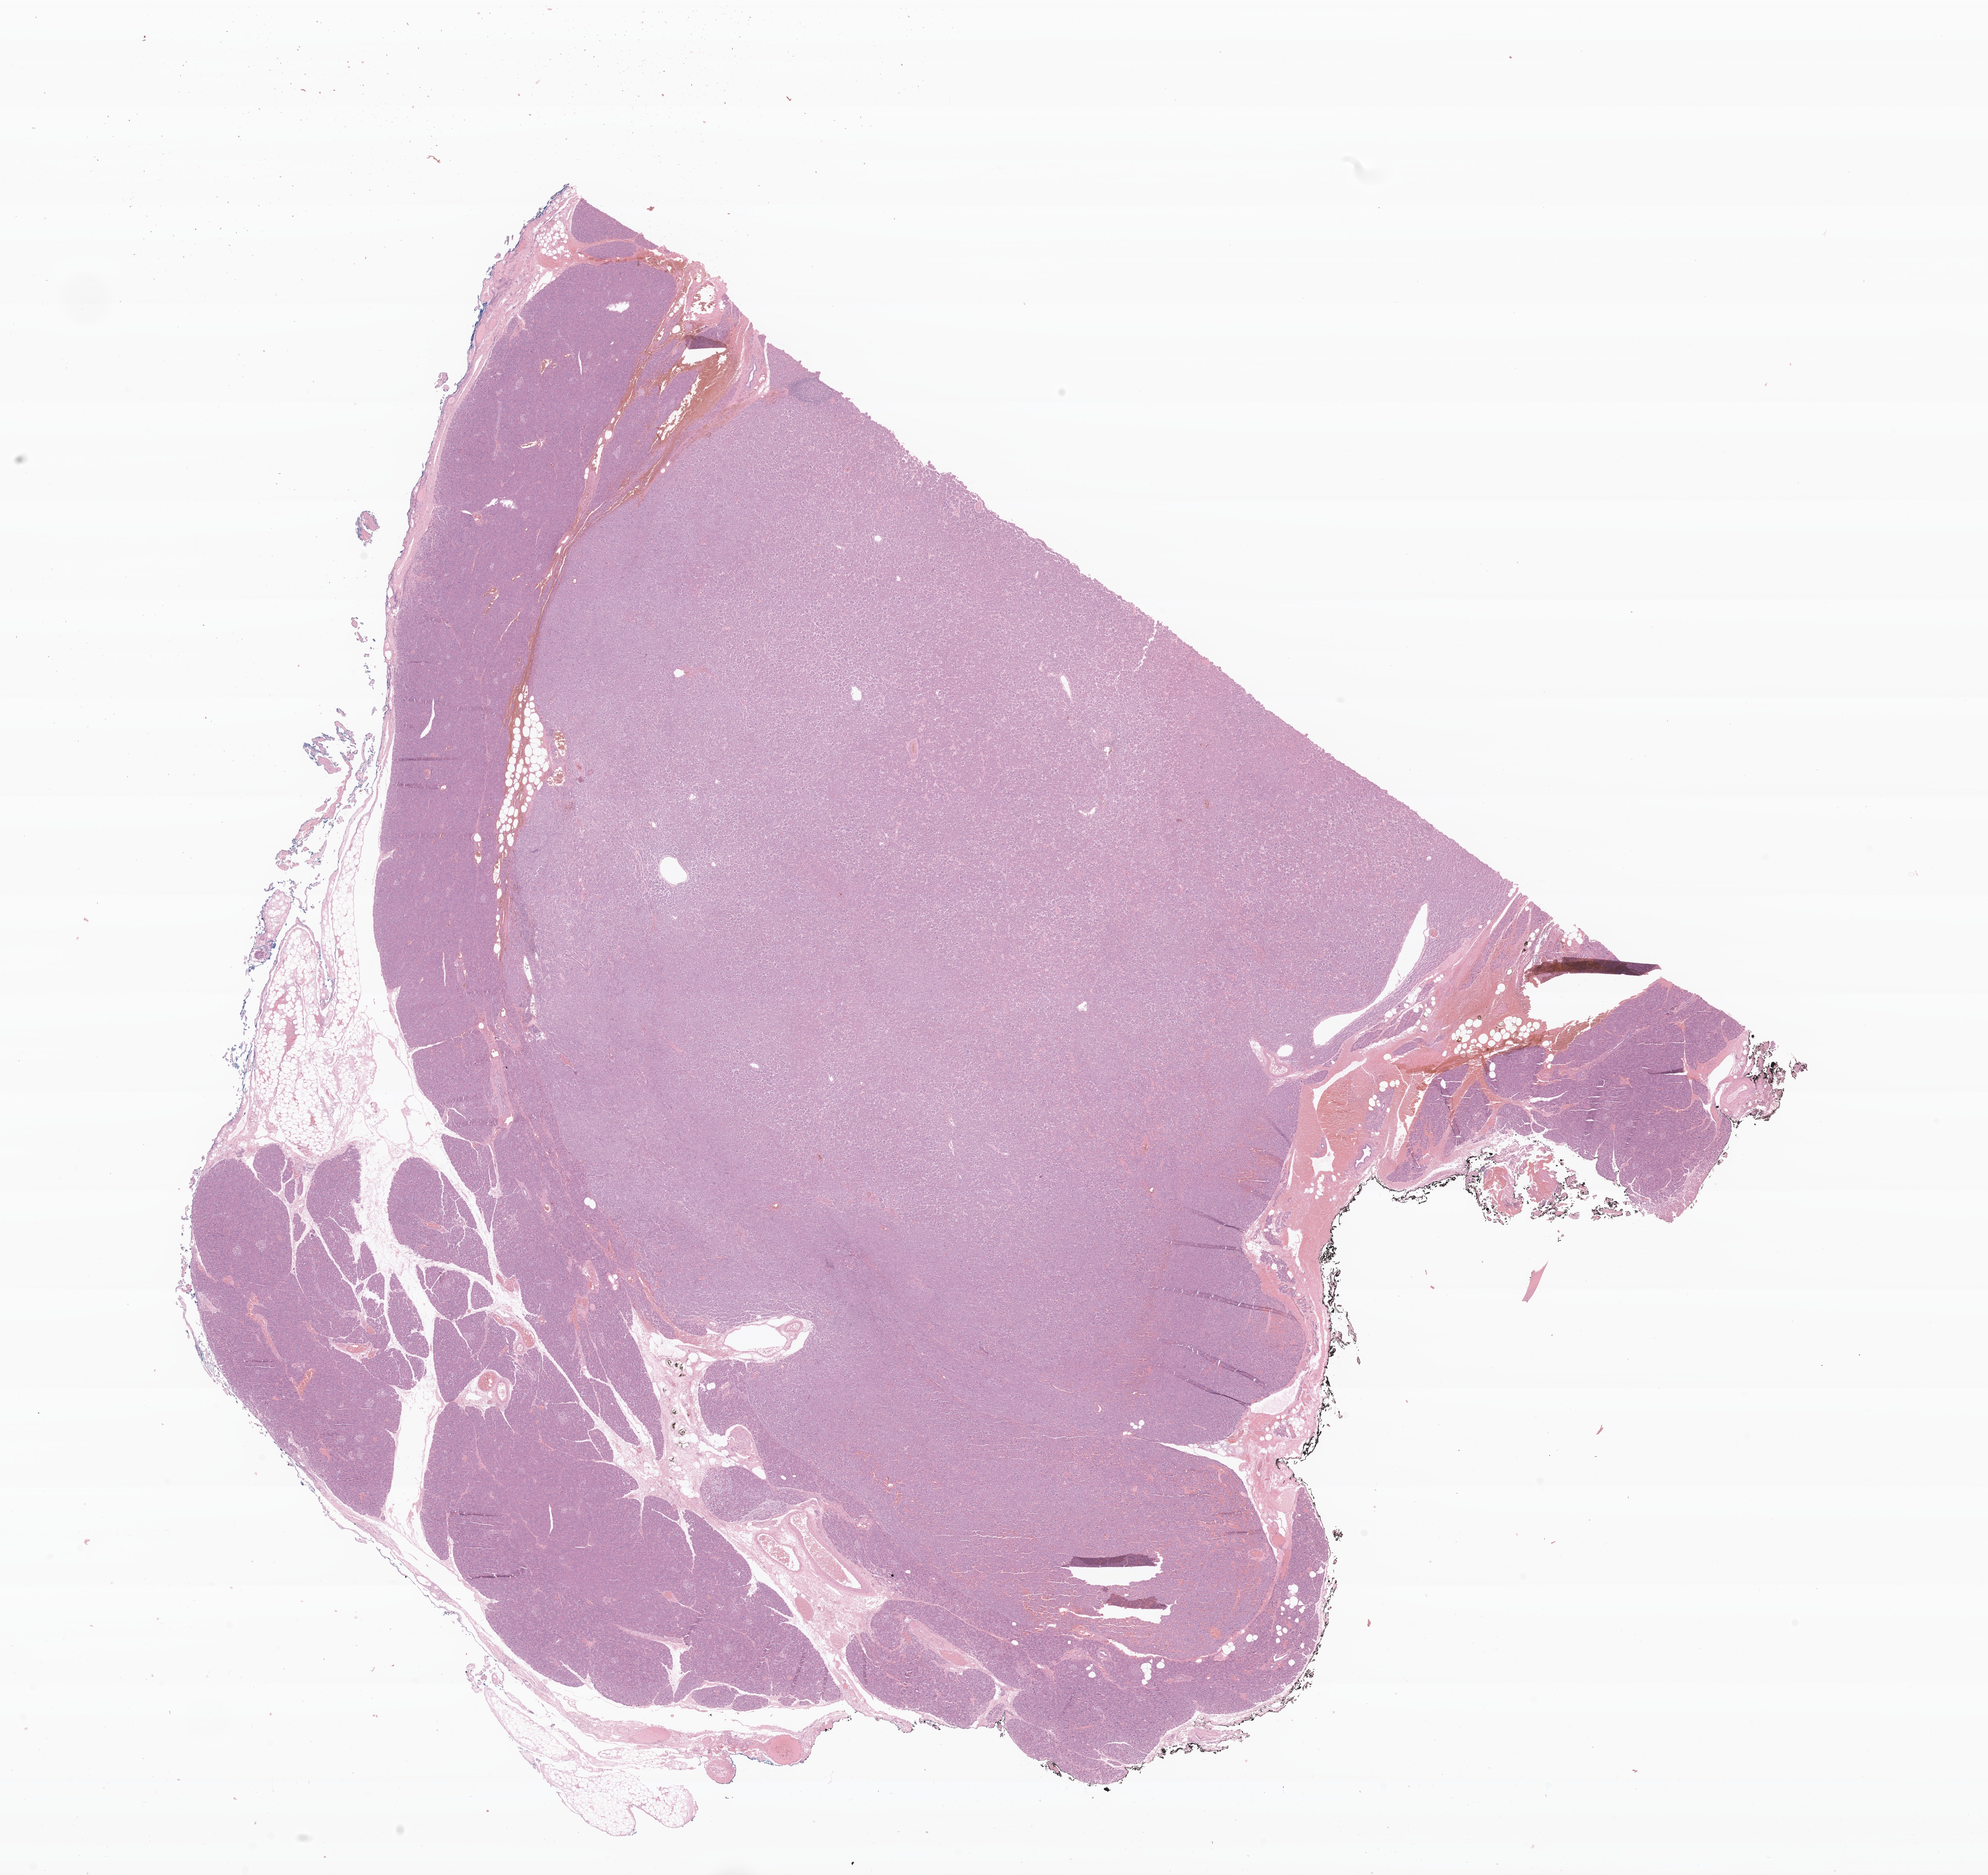
Digitized hematoxylin and eosin (H&E)-stained section of tumor tissue from the body of pancreas — shown as a low-resolution overview of the whole scanned area (about 21.5 x 20.3 mm); FFPE section. Male patient, age 125 months (10 years 5 months).
Diagnosis: Acinar cell carcinoma.